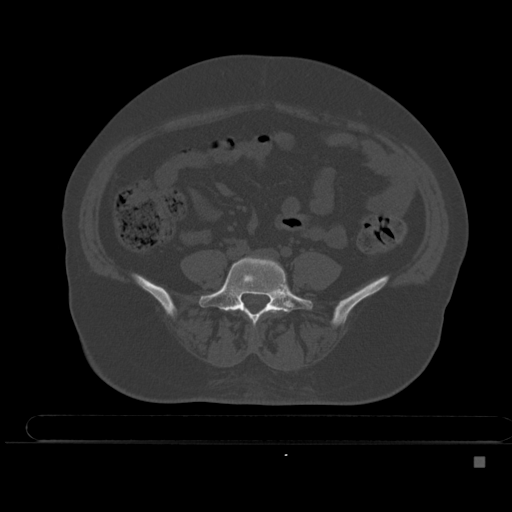
CT including the spine, one axial slice. Position 114 of 495 along the scan axis. Bone window (W 1800 / L 400 HU). 1.5 mm slice thickness. 512 × 512 image matrix, field of view 404 × 404 mm. Female patient, age 33 years. From the clinical record (not read from this slice): primary cancer: breast.
Outlined on this slice (semi-automatically segmented with operator editing):
- L4 vertebra: bounding box (x1, y1, x2, y2) in pixels: (239, 309, 278, 314)
- L5 vertebra: (199, 257, 313, 322)